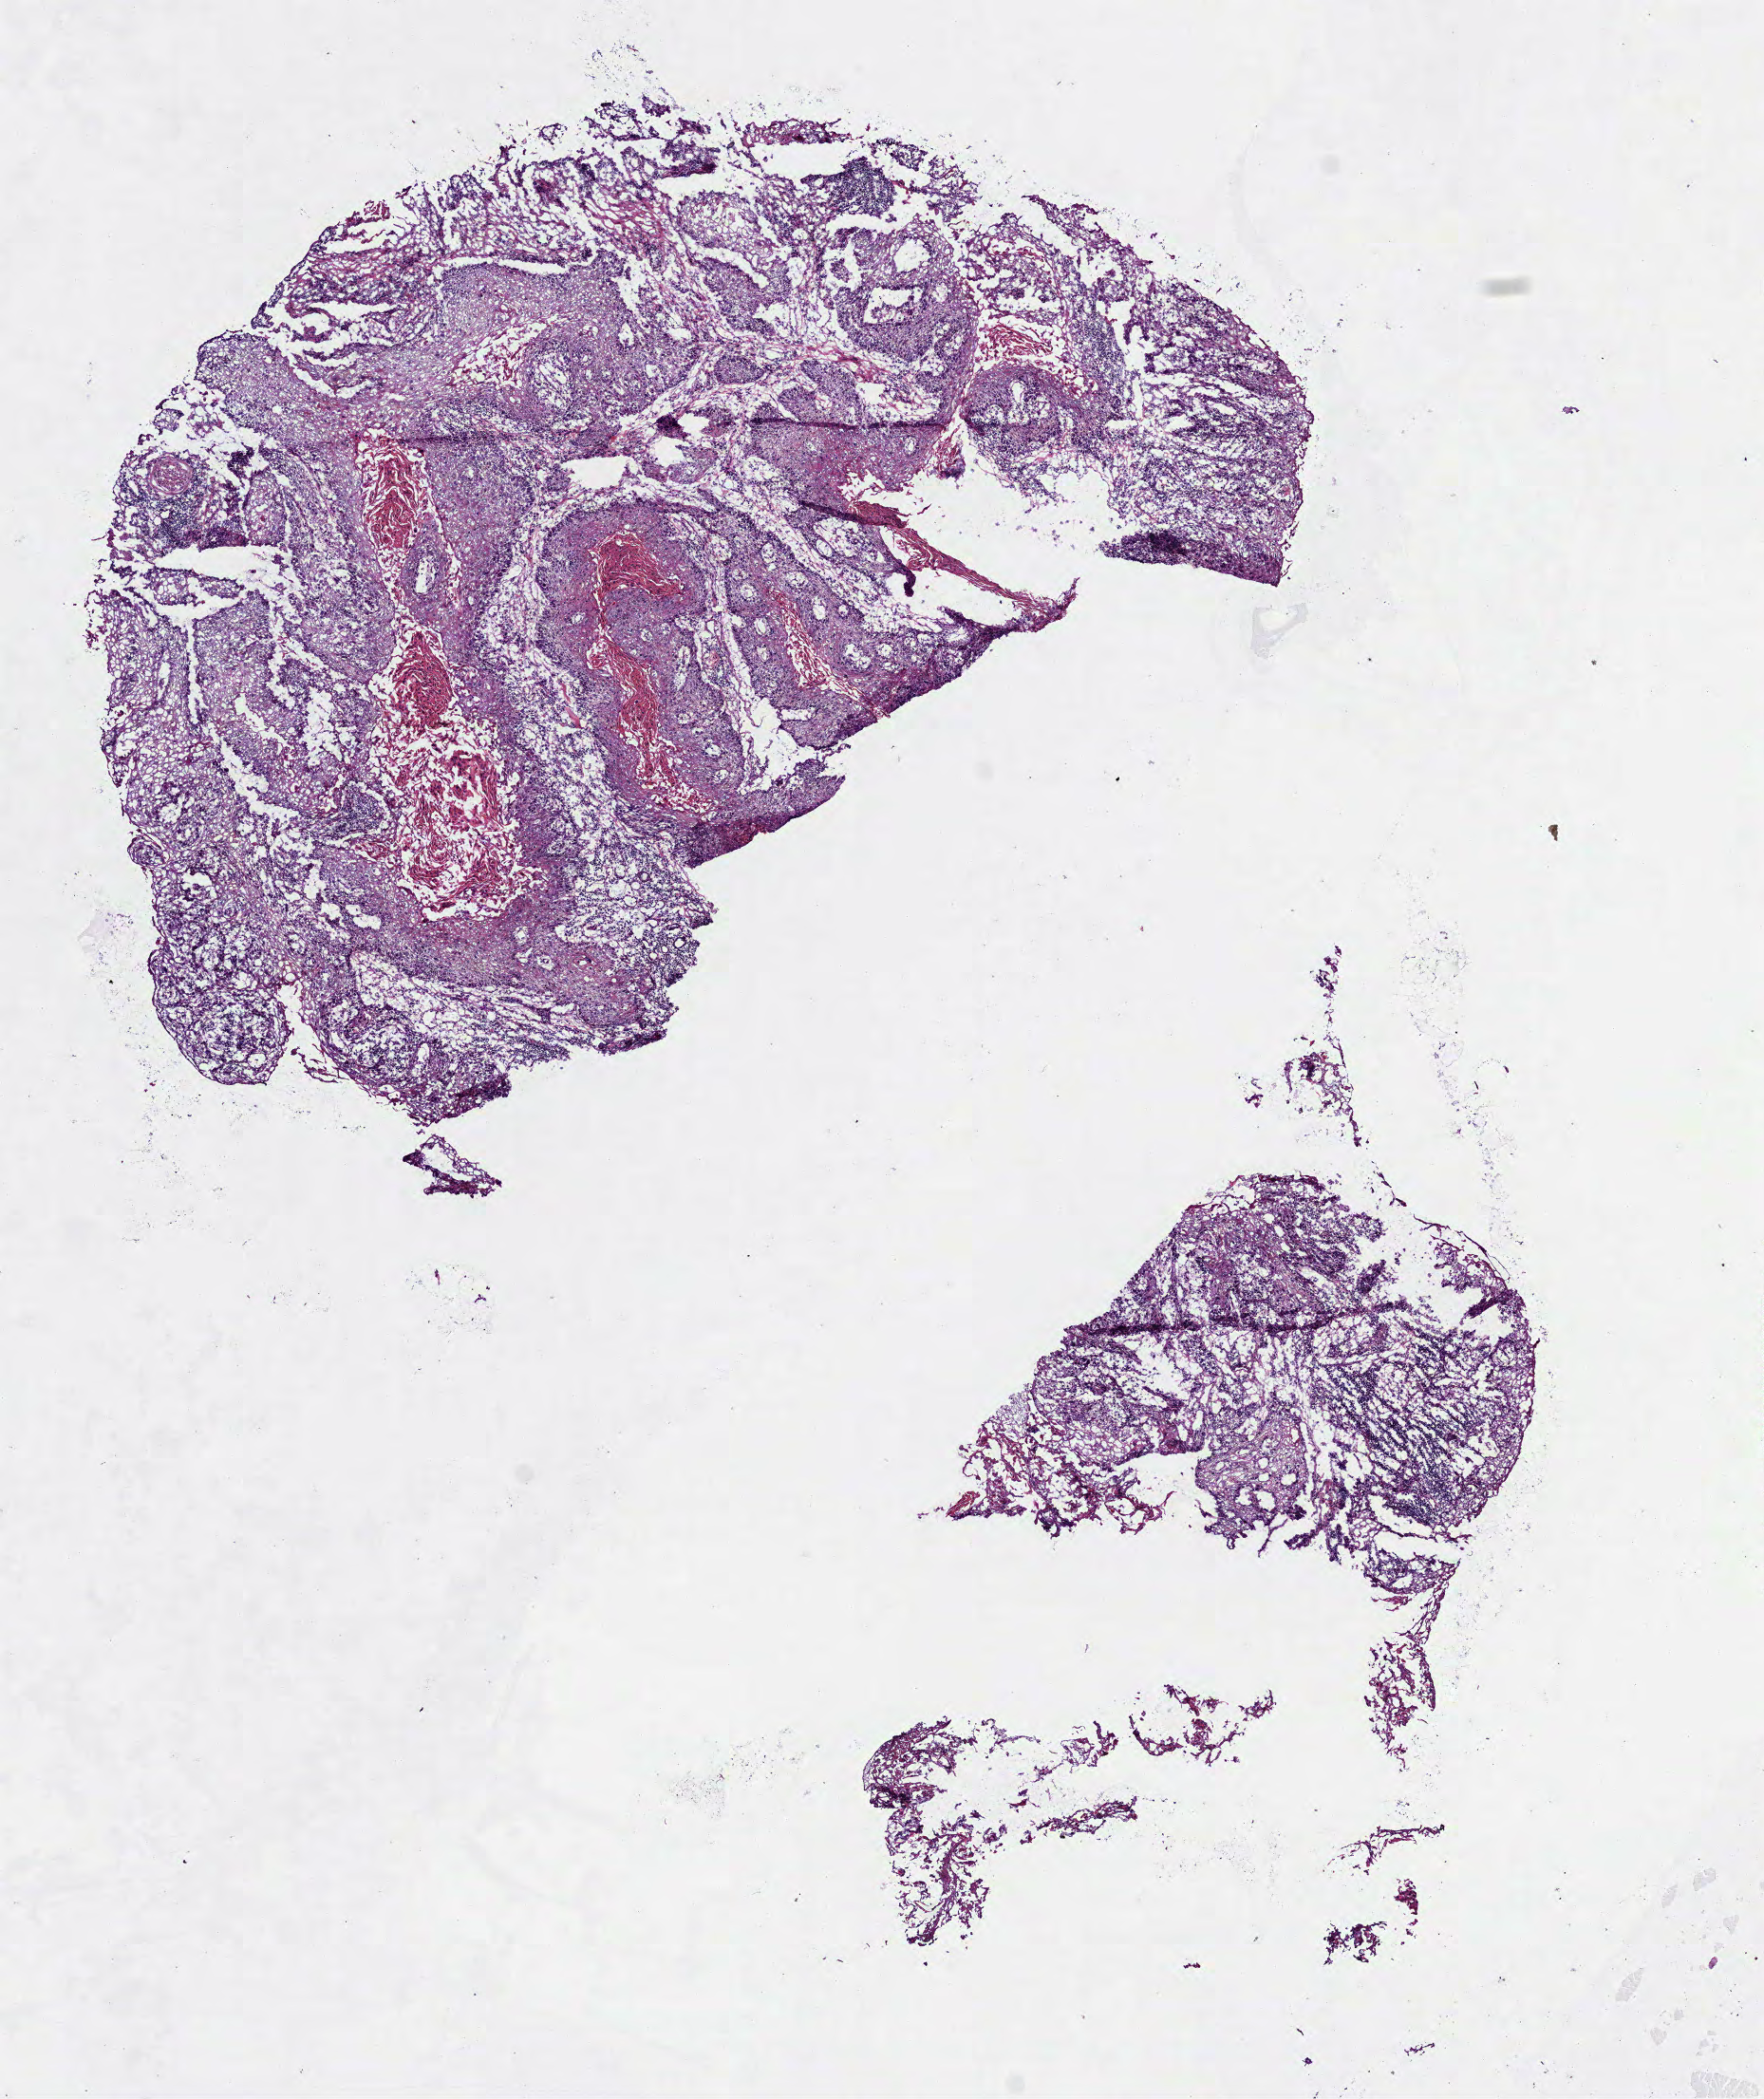
Whole-slide histology image, Hematoxylin and eosin (H&E) stained, a low-resolution overview of the entire scanned area, about 7.5 x 8.9 mm, frozen section from the bottom of the tissue portion, primary tumour sample from the head and neck. Female, age 63 years at initial diagnosis. Histologic grade: G2 (moderately differentiated). Composition of this section per pathologist review: tumour cells 85%, tumour nuclei 75%, normal cells 0%, stromal cells 15%, necrosis 0%.
Histologic diagnosis: Squamous cell carcinoma, NOS.